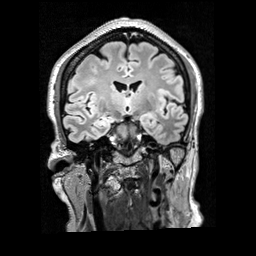
Brain MRI from a brain-tumour surgery series, one coronal slice; slice 104 of 200 in the series (ordered by position); T2 FLAIR; 256 × 256 image matrix, field of view 256 × 256 mm. Case-level facts recorded for this patient, not image findings: histopathology: Glioblastoma; WHO grade: 4; IDH mutation: no; tumour location: Right Frontal.
Structures marked on this image (manually delineated by an expert):
- tumour: box from (x=88, y=79) to (x=96, y=84) px